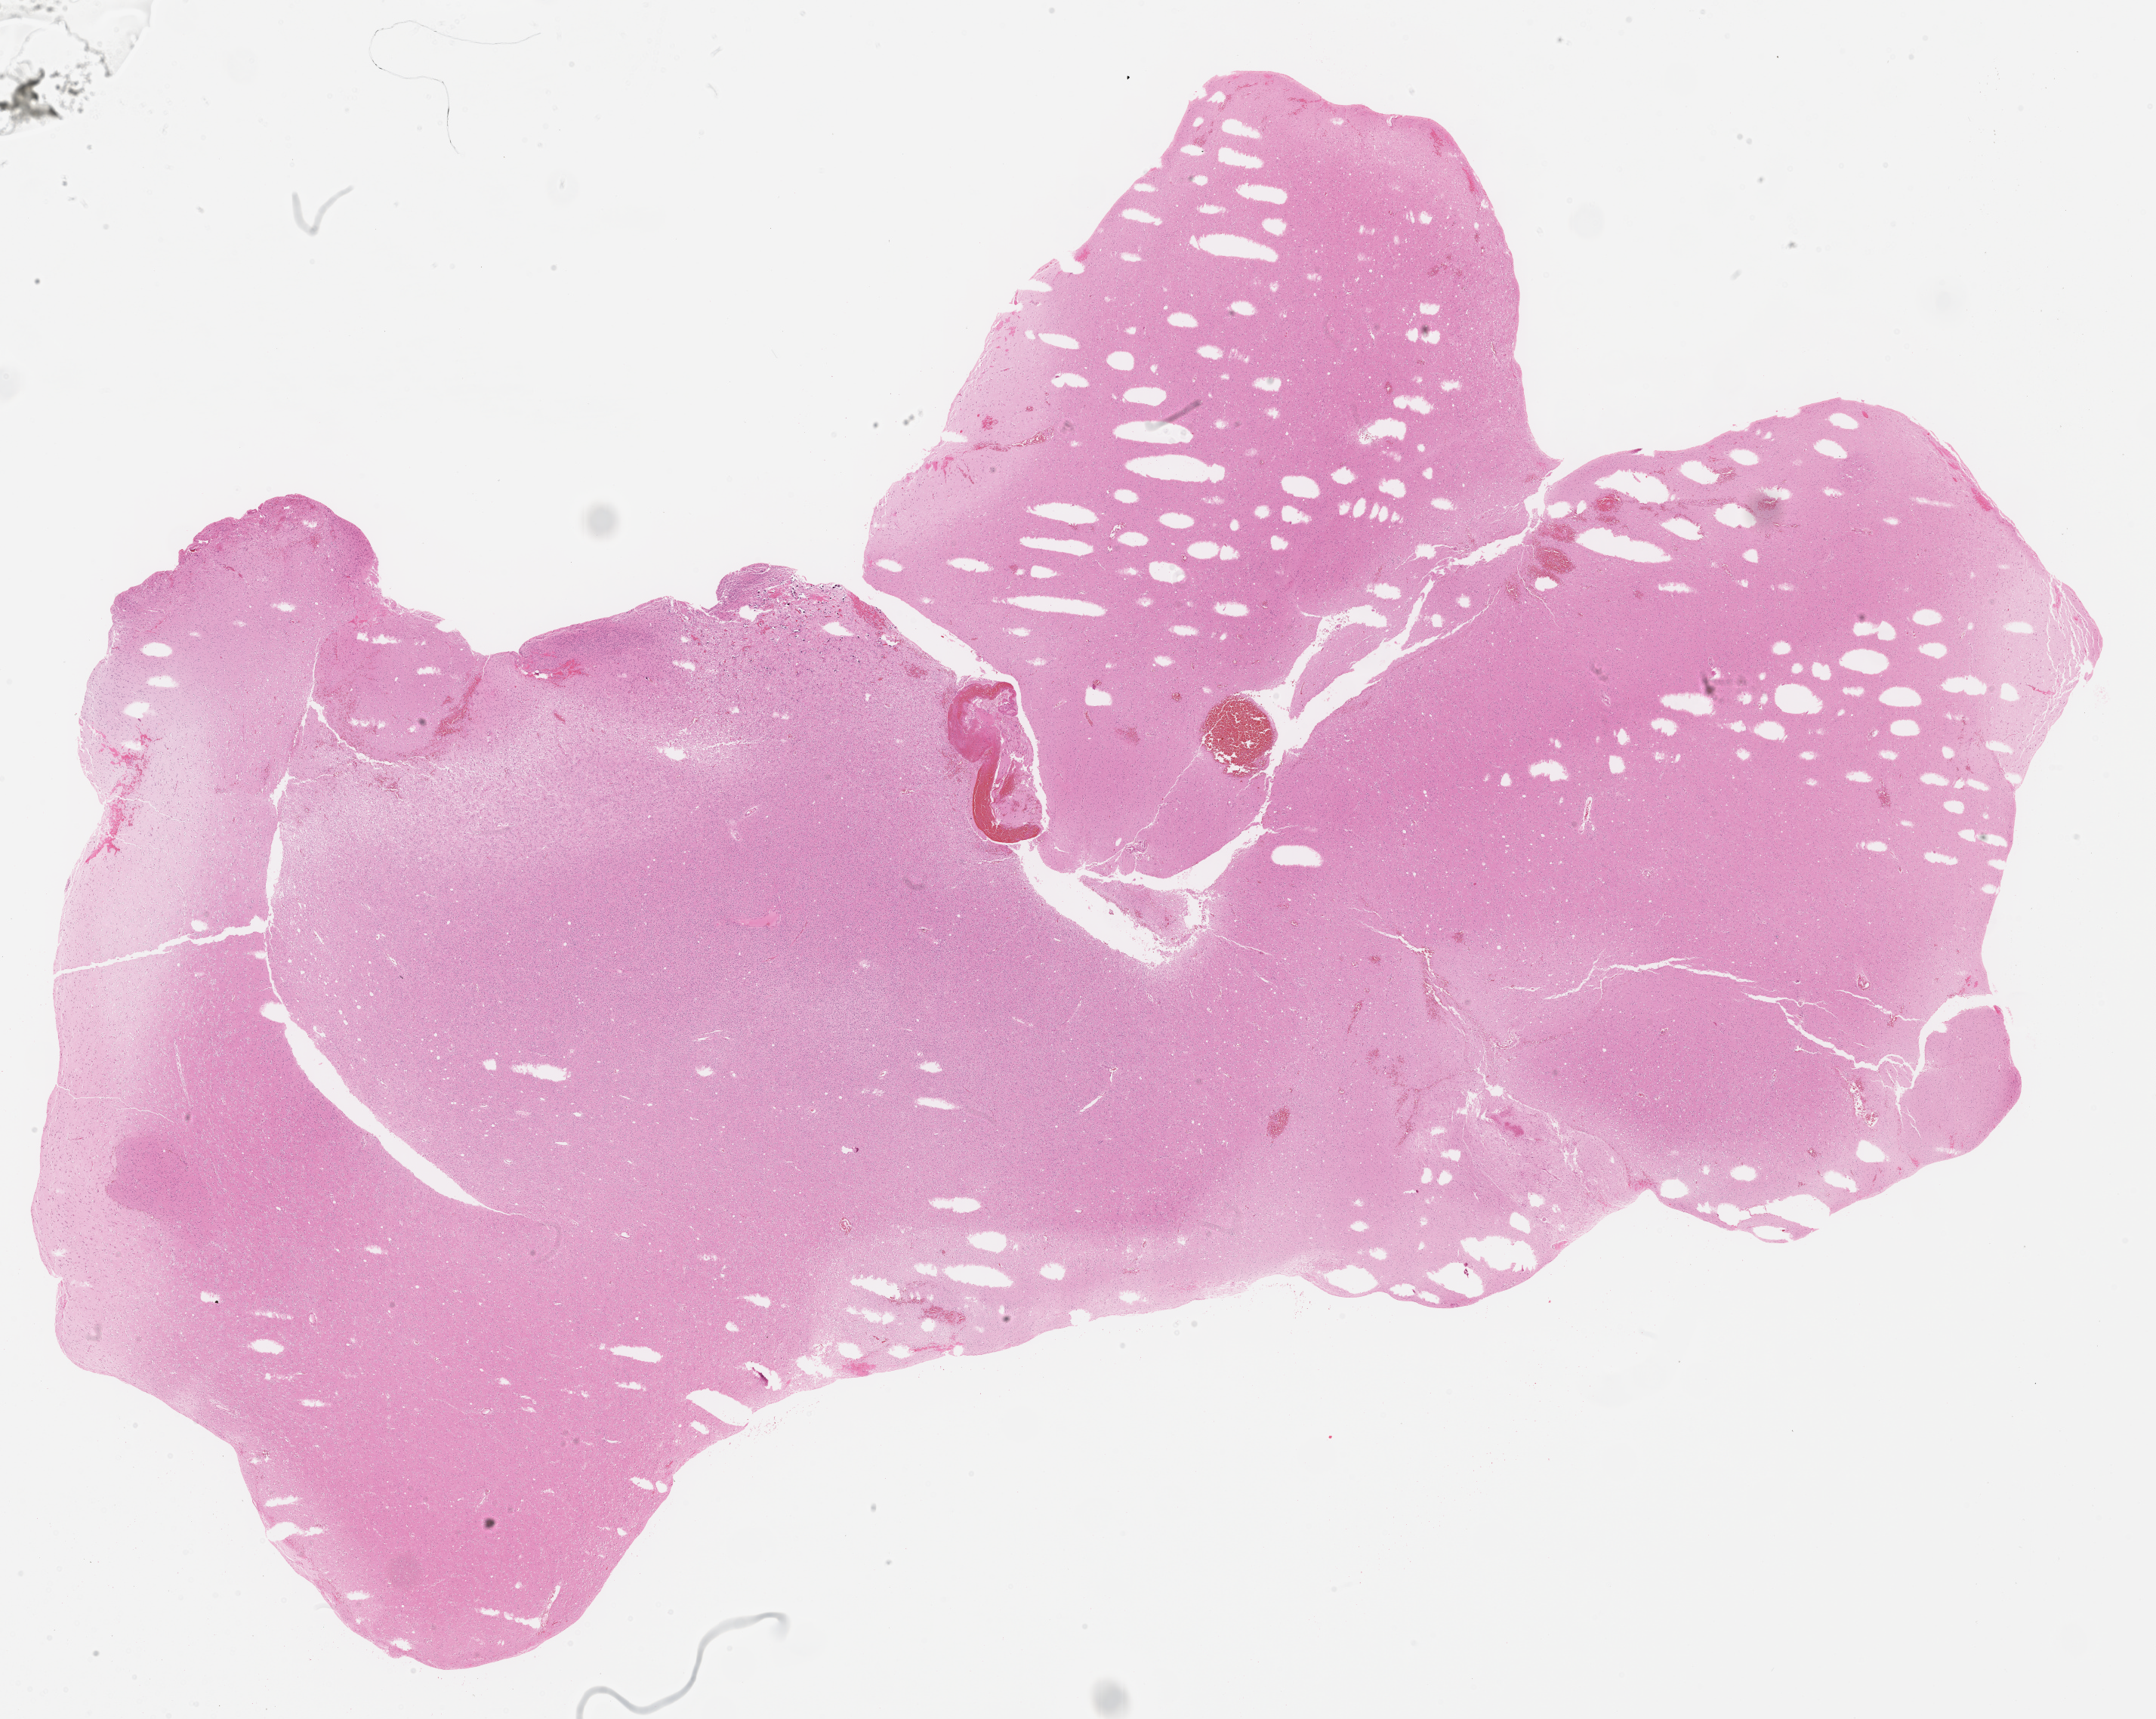
H&E-stained whole-slide image, shown as a low-resolution overview of the whole scanned area (about 23.0 x 18.3 mm). Formalin-fixed paraffin-embedded (FFPE) diagnostic section. Sample: primary tumour, brain. Patient: male, age at initial diagnosis 40 years. Histologic grade: G2 (moderately differentiated).
Laterality: right. Diagnosis: Oligodendroglioma, NOS.